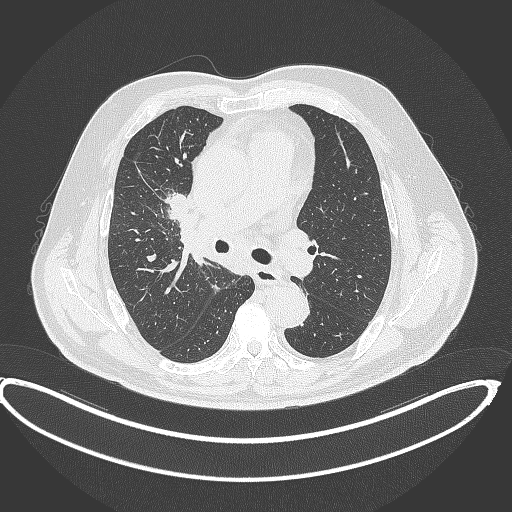
Chest CT, one axial slice. 120 kVp. Lung window (W 1500 / L -600 HU). 512 × 512 image matrix. Male patient, age 62 years. Case-level facts recorded for this patient, not image findings: clinical TNM (as recorded): T1c N3 M1c.
Annotated regions visible in this slice (bounding box drawn by a radiologist):
- lung tumour (recorded histology: adenocarcinoma): bounding box [x1, y1, x2, y2] px = [163, 189, 190, 220]